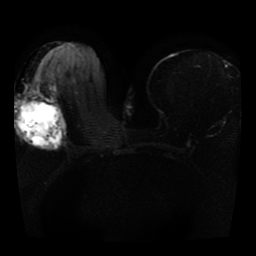
Breast MRI, one axial slice. Slice 19 of 41 in the series (ordered by position). Diffusion-weighted series; image 2 of 4 stored at this slice position (different b-values; order by instance number). 1.5 T. 5 mm slice thickness. 256 × 256 image matrix, field of view 330 × 330 mm. Female patient.
Annotated regions visible in this slice (expert manual segmentation):
- tumour on diffusion-weighted imaging: bounding box [x1, y1, x2, y2] px = [15, 96, 66, 132]